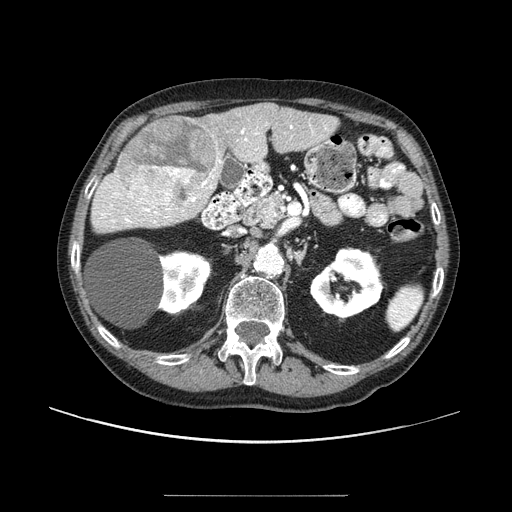
Contrast-enhanced abdominal CT (liver protocol), one axial slice. Position 44 of 91 along the scan axis. Reconstruction kernel STANDARD. 100 kVp. One of 2 acquisitions stored at this slice position. Soft-tissue window (W 400 / L 40 HU). 512 × 512 image matrix. Case-level facts recorded for this patient, not image findings: diagnosis: hepatocellular carcinoma (patient treated with transarterial chemoembolisation; whether this scan precedes or follows treatment is not stated here); TNM stage (as recorded): Stage-I; Child-Pugh class: A.
Annotated regions visible in this slice (semi-automatic segmentation, software-assisted and operator-edited):
- liver parenchyma outside the tumour (the mass and vessels are separate outlines, so this box may not span the whole liver): bounding box (x1, y1, x2, y2) in pixels: (94, 102, 338, 226)
- mass: (117, 116, 218, 212)
- liver vessels: (110, 126, 293, 224)